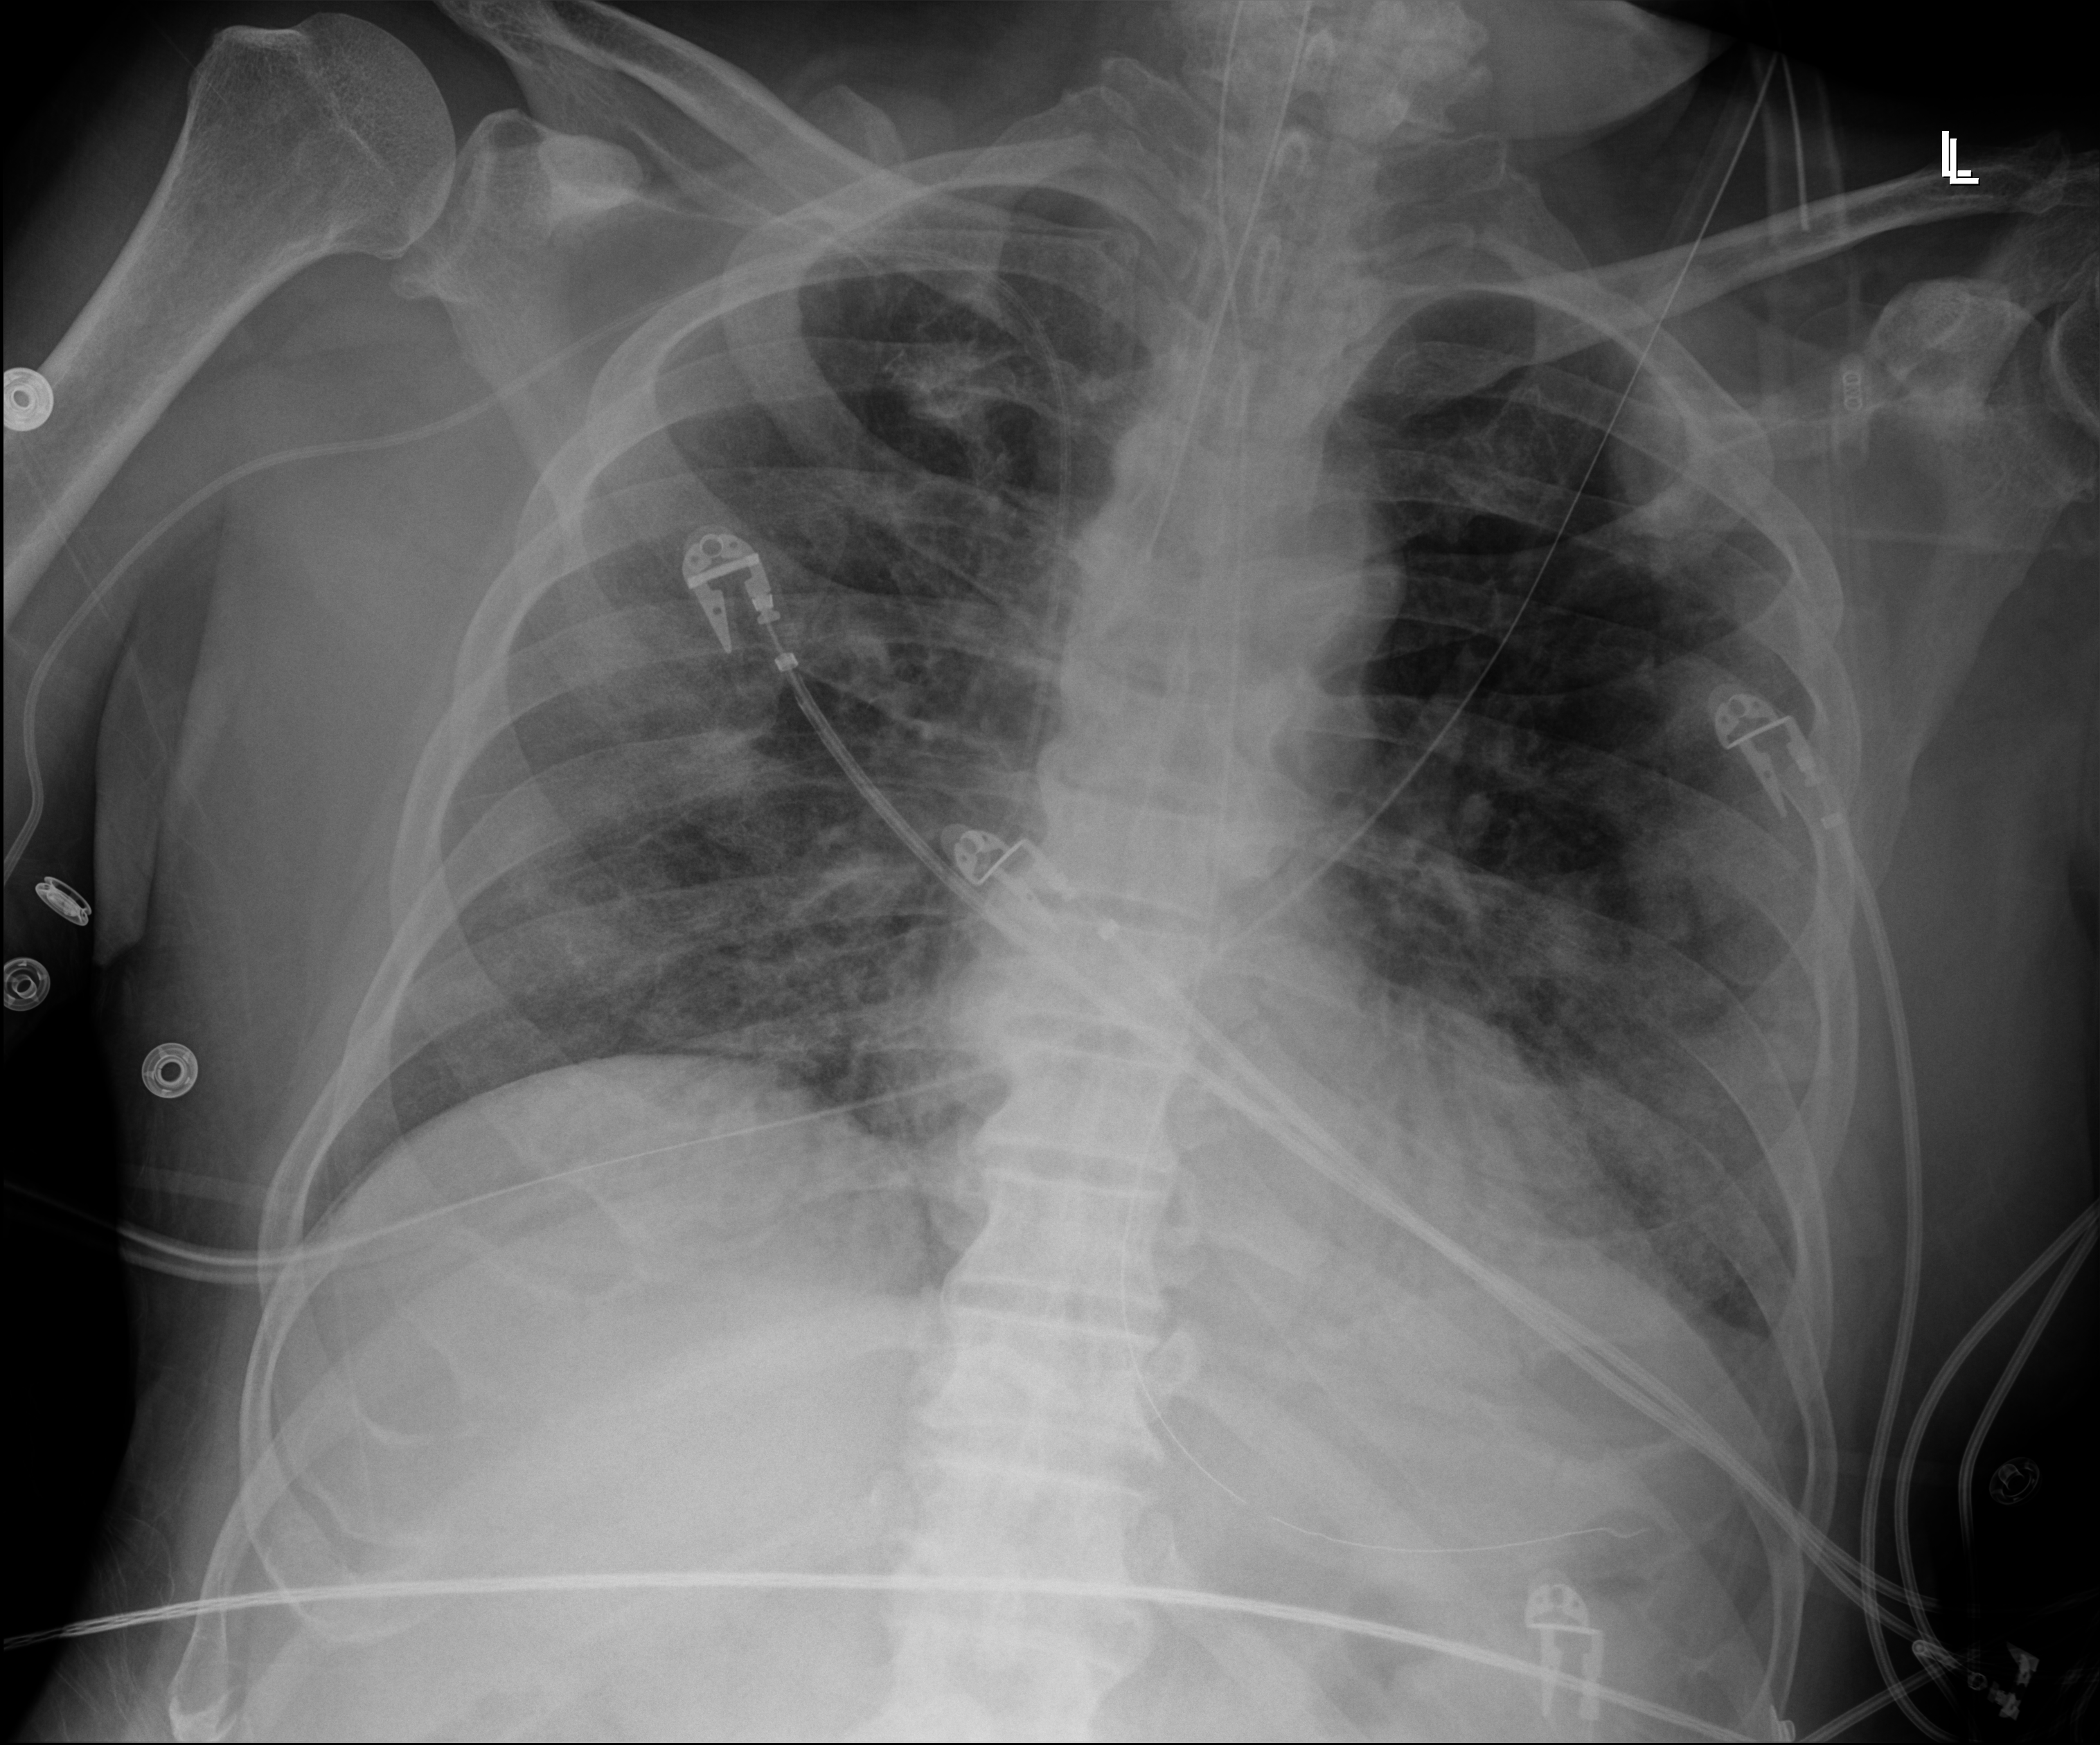
Portable chest radiograph, anteroposterior (AP) projection. Male patient hospitalised with COVID-19, age 75–90 years.
From the hospital-stay record, not from the radiograph (when in the stay this image was taken is not recorded): chronic kidney disease (admission record): no; mechanically ventilated during this hospital stay: yes; length of hospital stay: 33 days.